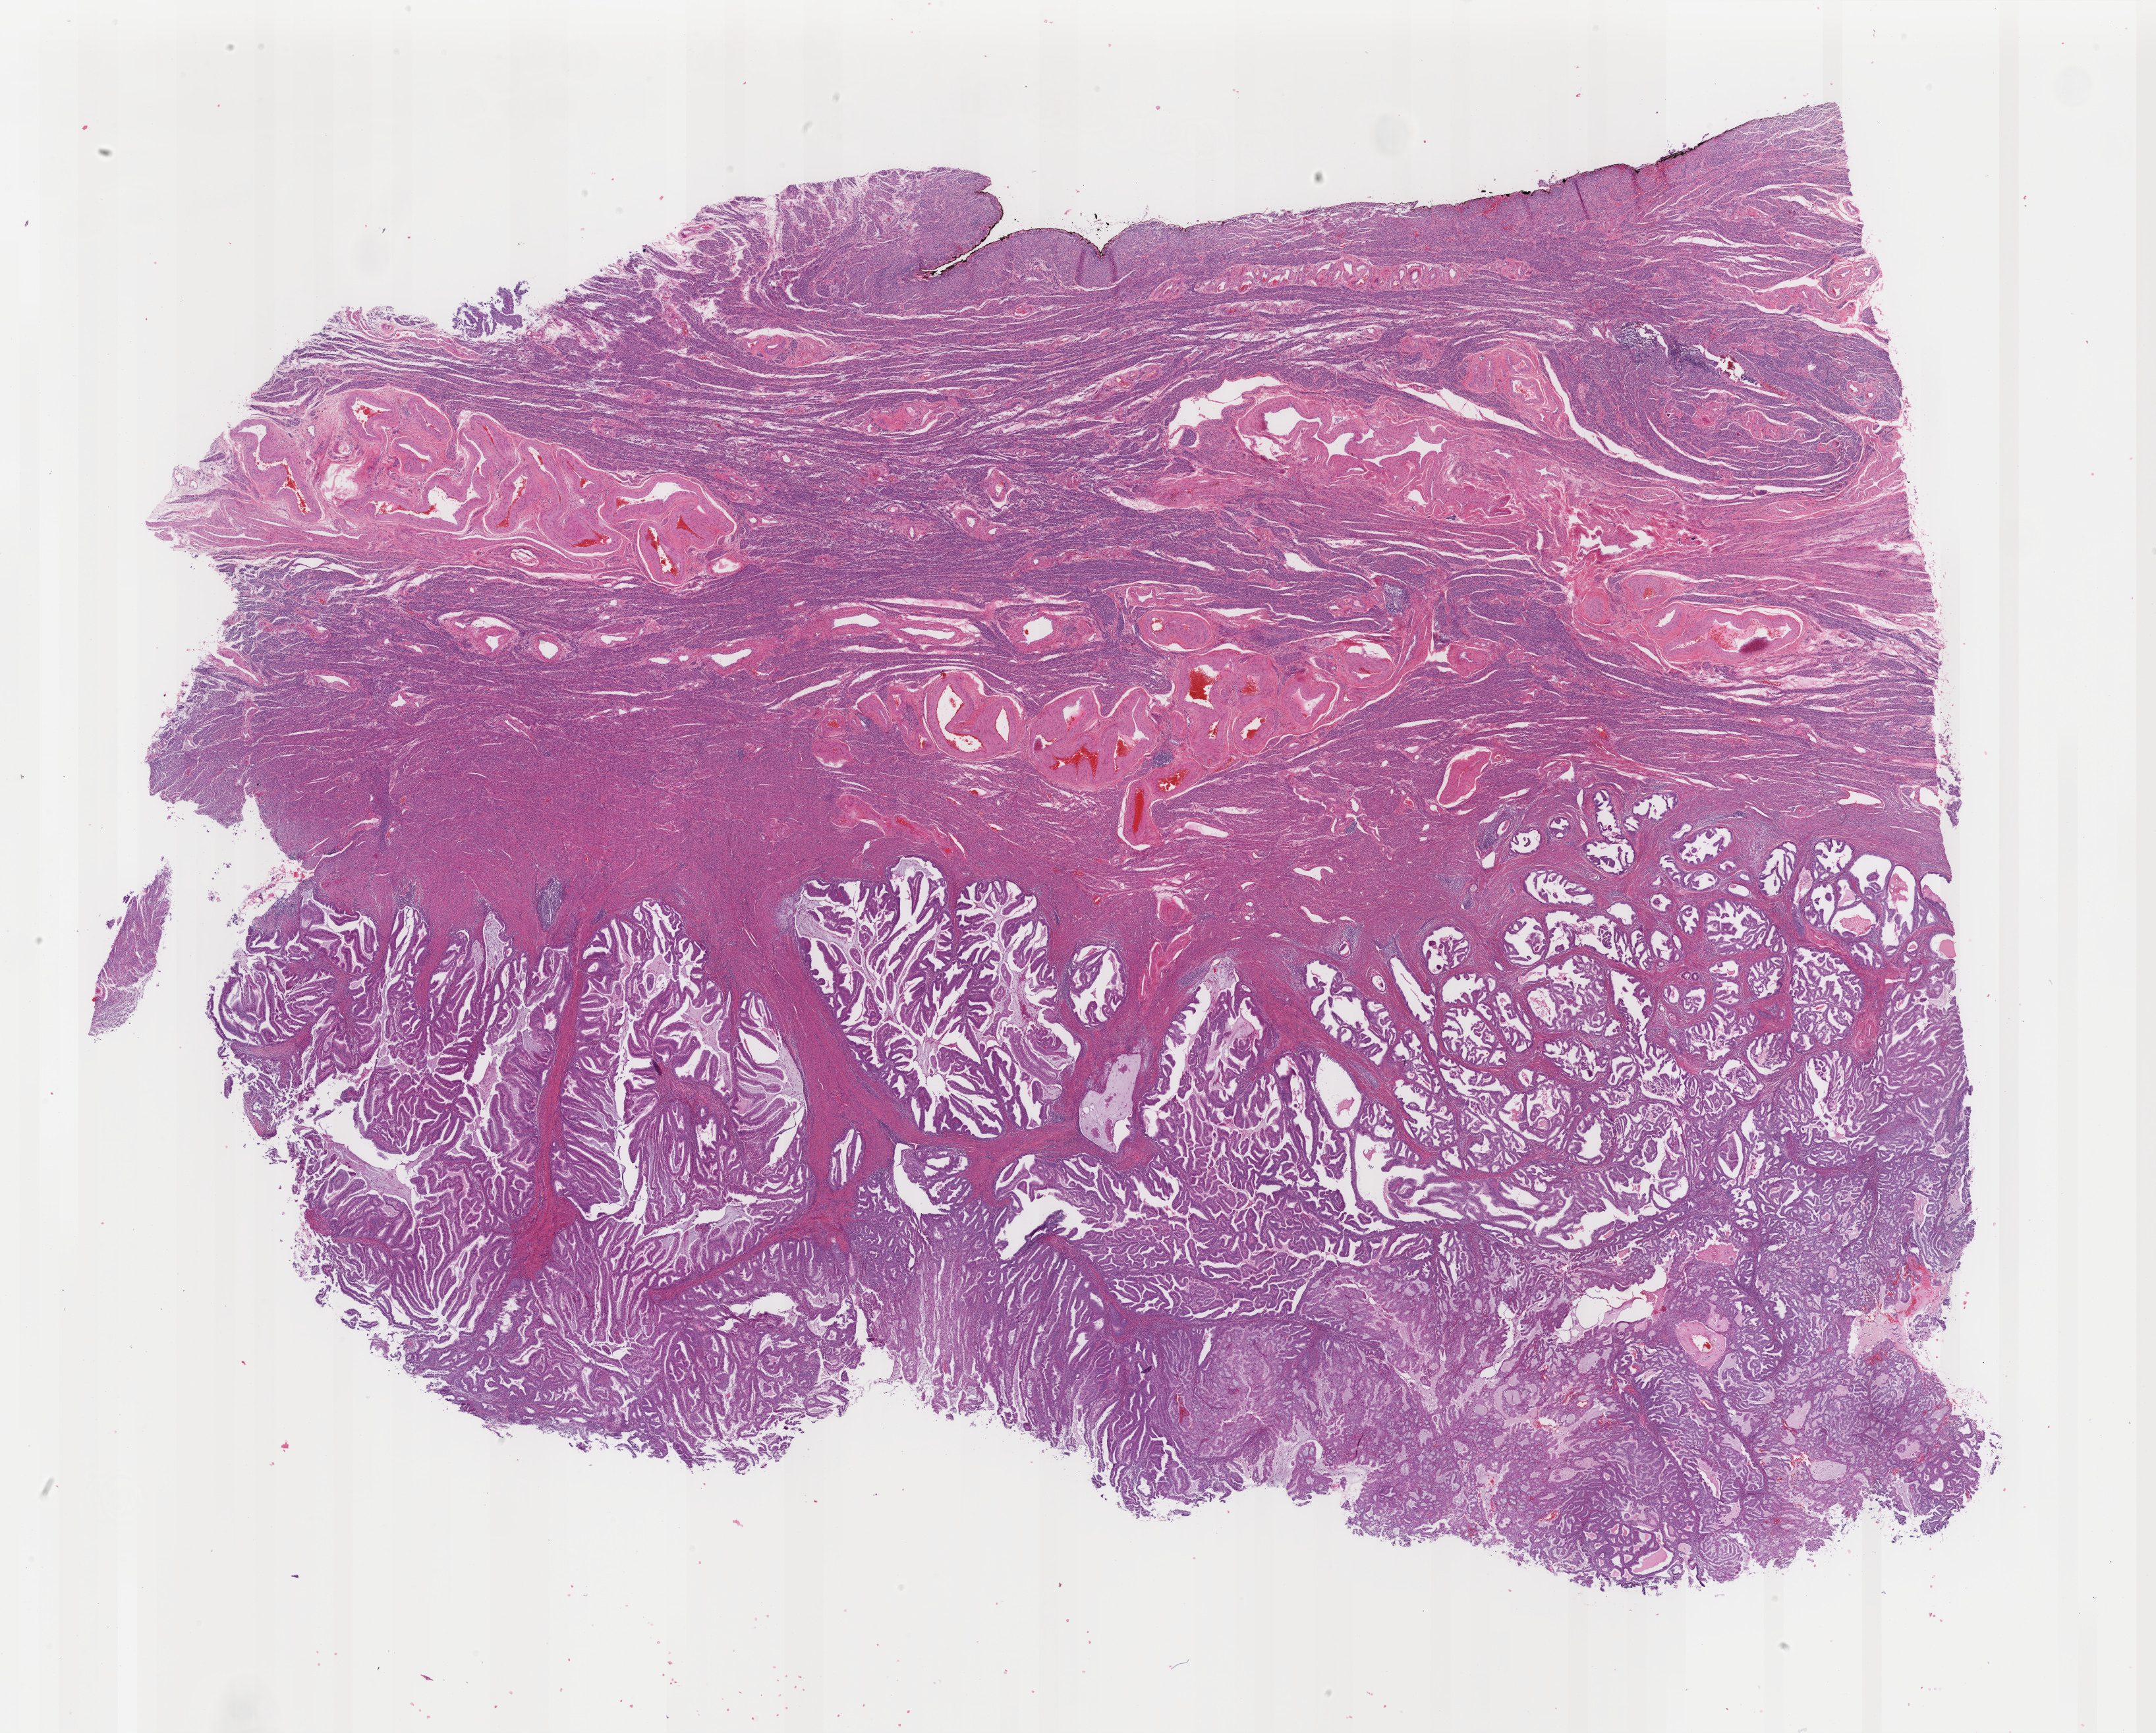
Digitized H&E-stained tissue section (whole slide), whole scanned area (about 26.0 x 20.9 mm, slide scanned at 40x) shown as a low-resolution overview. FFPE section. Uterus, primary tumour sample. Female, age 59 years at initial diagnosis. Histologic grade: G1 (well differentiated).
• FIGO stage: IB
• diagnosis: Endometrioid adenocarcinoma, secretory variant (endometrium)